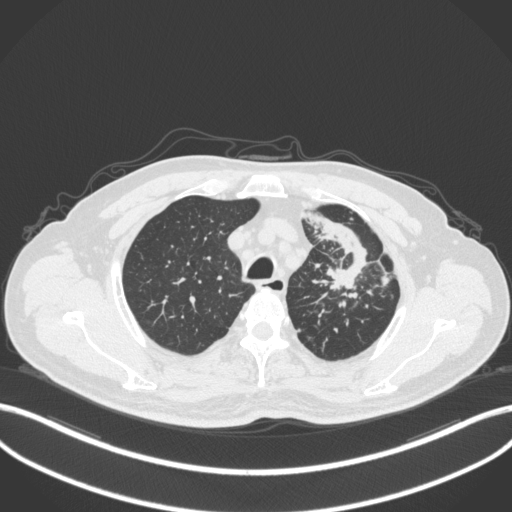
Chest CT, one axial slice; position 289 of 386 along the scan axis; reconstruction kernel B31f; 120 kVp; lung window (W 1500 / L -600 HU); 1 mm slice thickness; 512 × 512 image matrix, field of view 400 × 400 mm. Male patient, age 69 years. From the clinical record (not read from this slice): clinical TNM (as recorded): T2a N2 M0.
Outlined on this slice (bounding box drawn by a radiologist):
- lung tumour (recorded histology: adenocarcinoma): bounding box (x1, y1, x2, y2) in pixels: (305, 209, 368, 297)